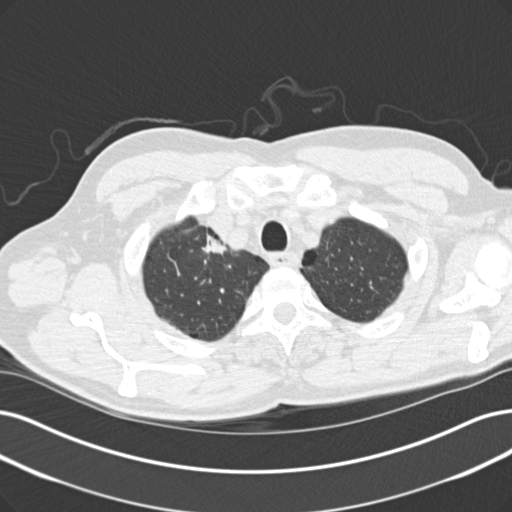
Low-dose screening chest CT, one axial slice. Position 129 of 152 along the scan axis. Reconstruction kernel B30f. 120 kVp. Lung window (W 1500 / L -600 HU). 2 mm slice thickness. 512 × 512 image matrix, field of view 365 × 365 mm.
Structures marked on this image (manually delineated by an expert):
- lesion 1 (tumor, upper lobe of right lung): box from (x=202, y=234) to (x=227, y=254) px